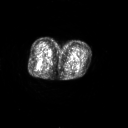
FDG PET of an extremity soft-tissue mass (from a PET/CT study), one axial slice; position 23 of 267 along the scan axis; 3.27 mm slice thickness; 128 × 128 image matrix, field of view 700 × 700 mm. Female patient, age 70 years. From the clinical record (not read from this slice): histological type: synovial sarcoma; grade: intermediate; site of the primary tumour: right buttock.
Annotated regions visible in this slice (expert contour drawn on MRI and transferred to this co-registered scan by the dataset authors):
- gross tumour volume including surrounding oedema: bounding box (x1, y1, x2, y2) in pixels: (34, 60, 39, 68)